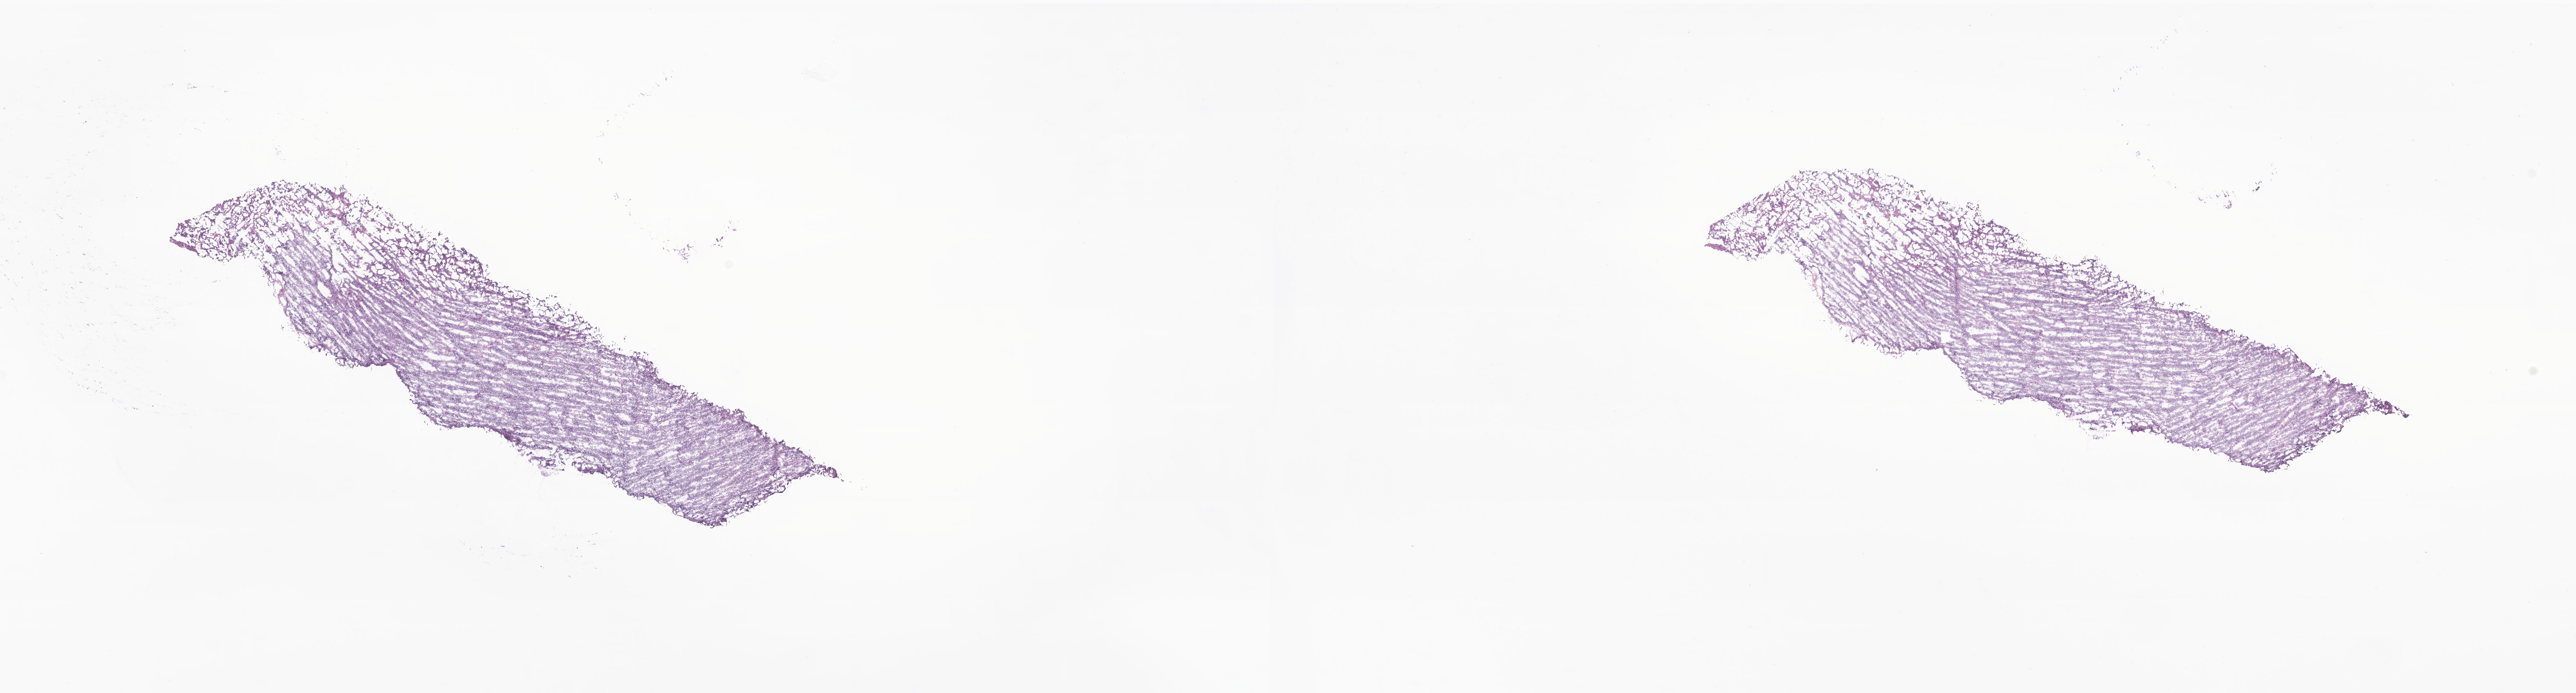
Whole-slide image, haematoxylin and eosin stain of tumor tissue from the brain, low-resolution overview of the scanned area, about 28.2 x 7.6 mm; cryosection (OCT / tissue freezing medium). Patient: male, age 91 months (7 years 7 months).
* recorded diagnosis: Medulloblastoma, NOS